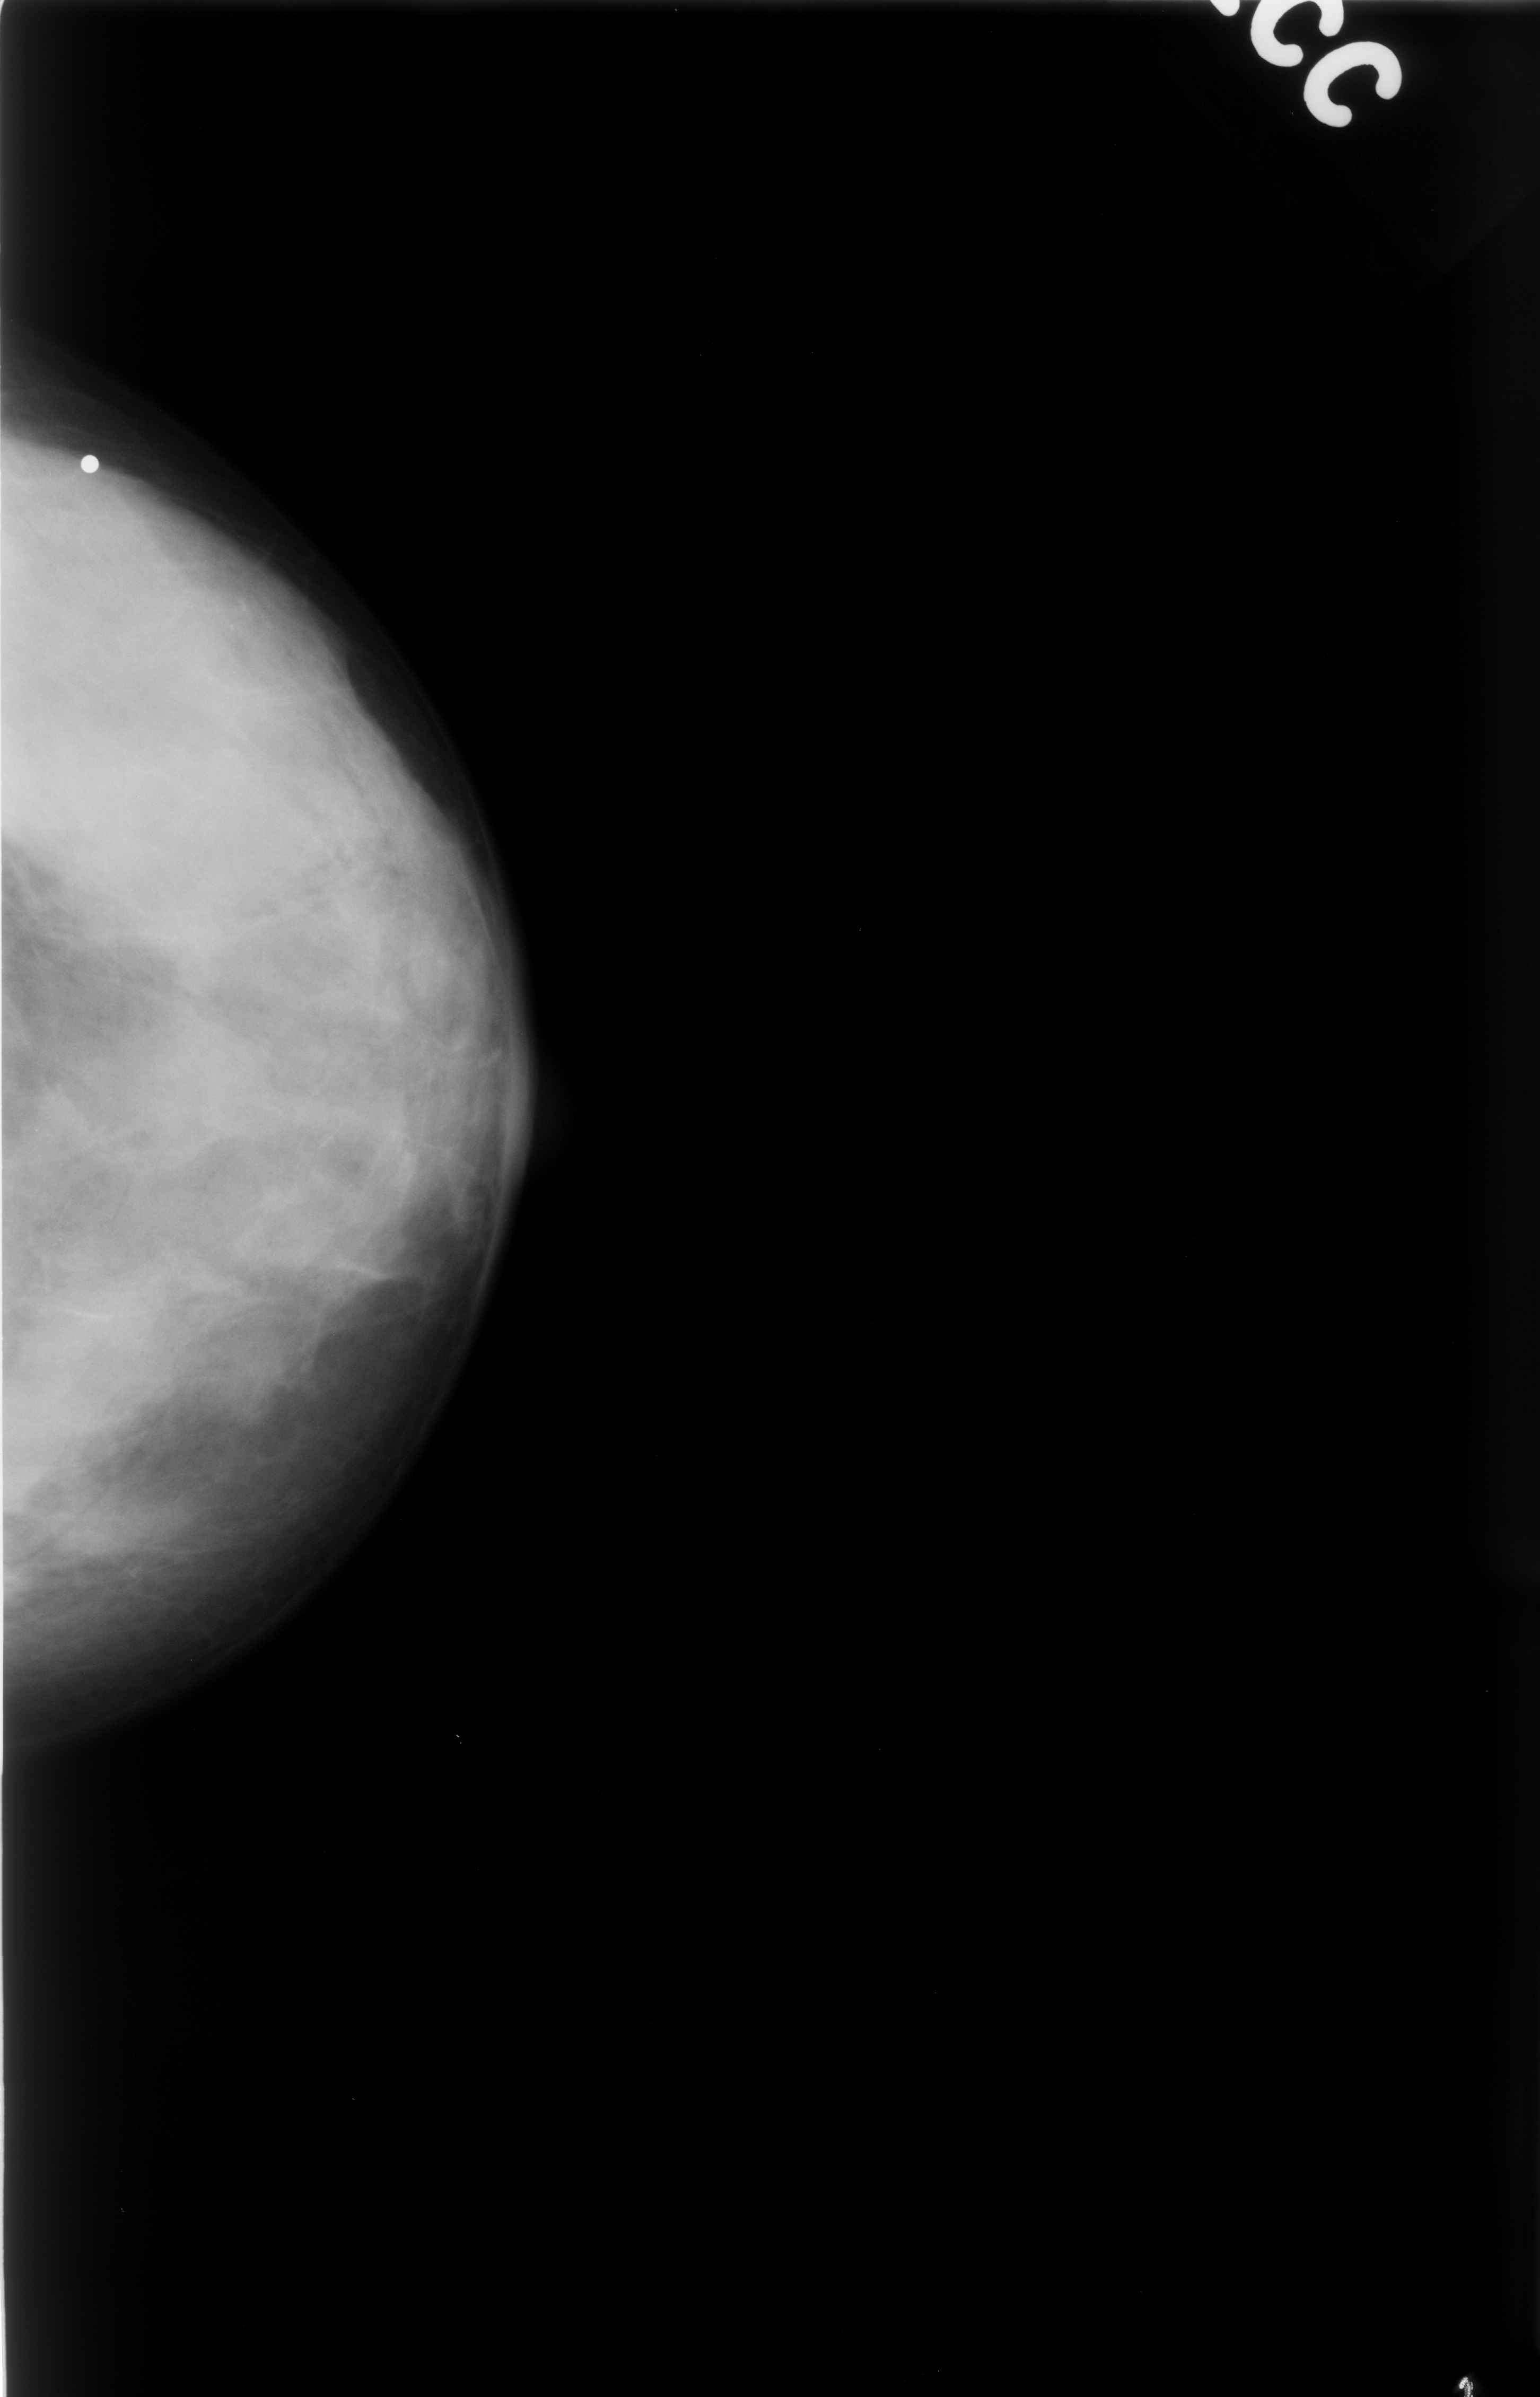
Scanned film-screen mammogram; left breast; CC view; BI-RADS breast density category 4 (scale 1–4); 1540 × 2397 image matrix.
Expert-marked regions of interest on this image (one box per marked abnormality):
- calcifications, morphology amorphous, distribution clustered; BI-RADS assessment category 4; subtlety rating 3 on a 1 (subtle) to 5 (obvious) scale; pathology result (as recorded, not read from the image): benign: bounding box <144,538,328,680> (left, top, right, bottom; pixels)